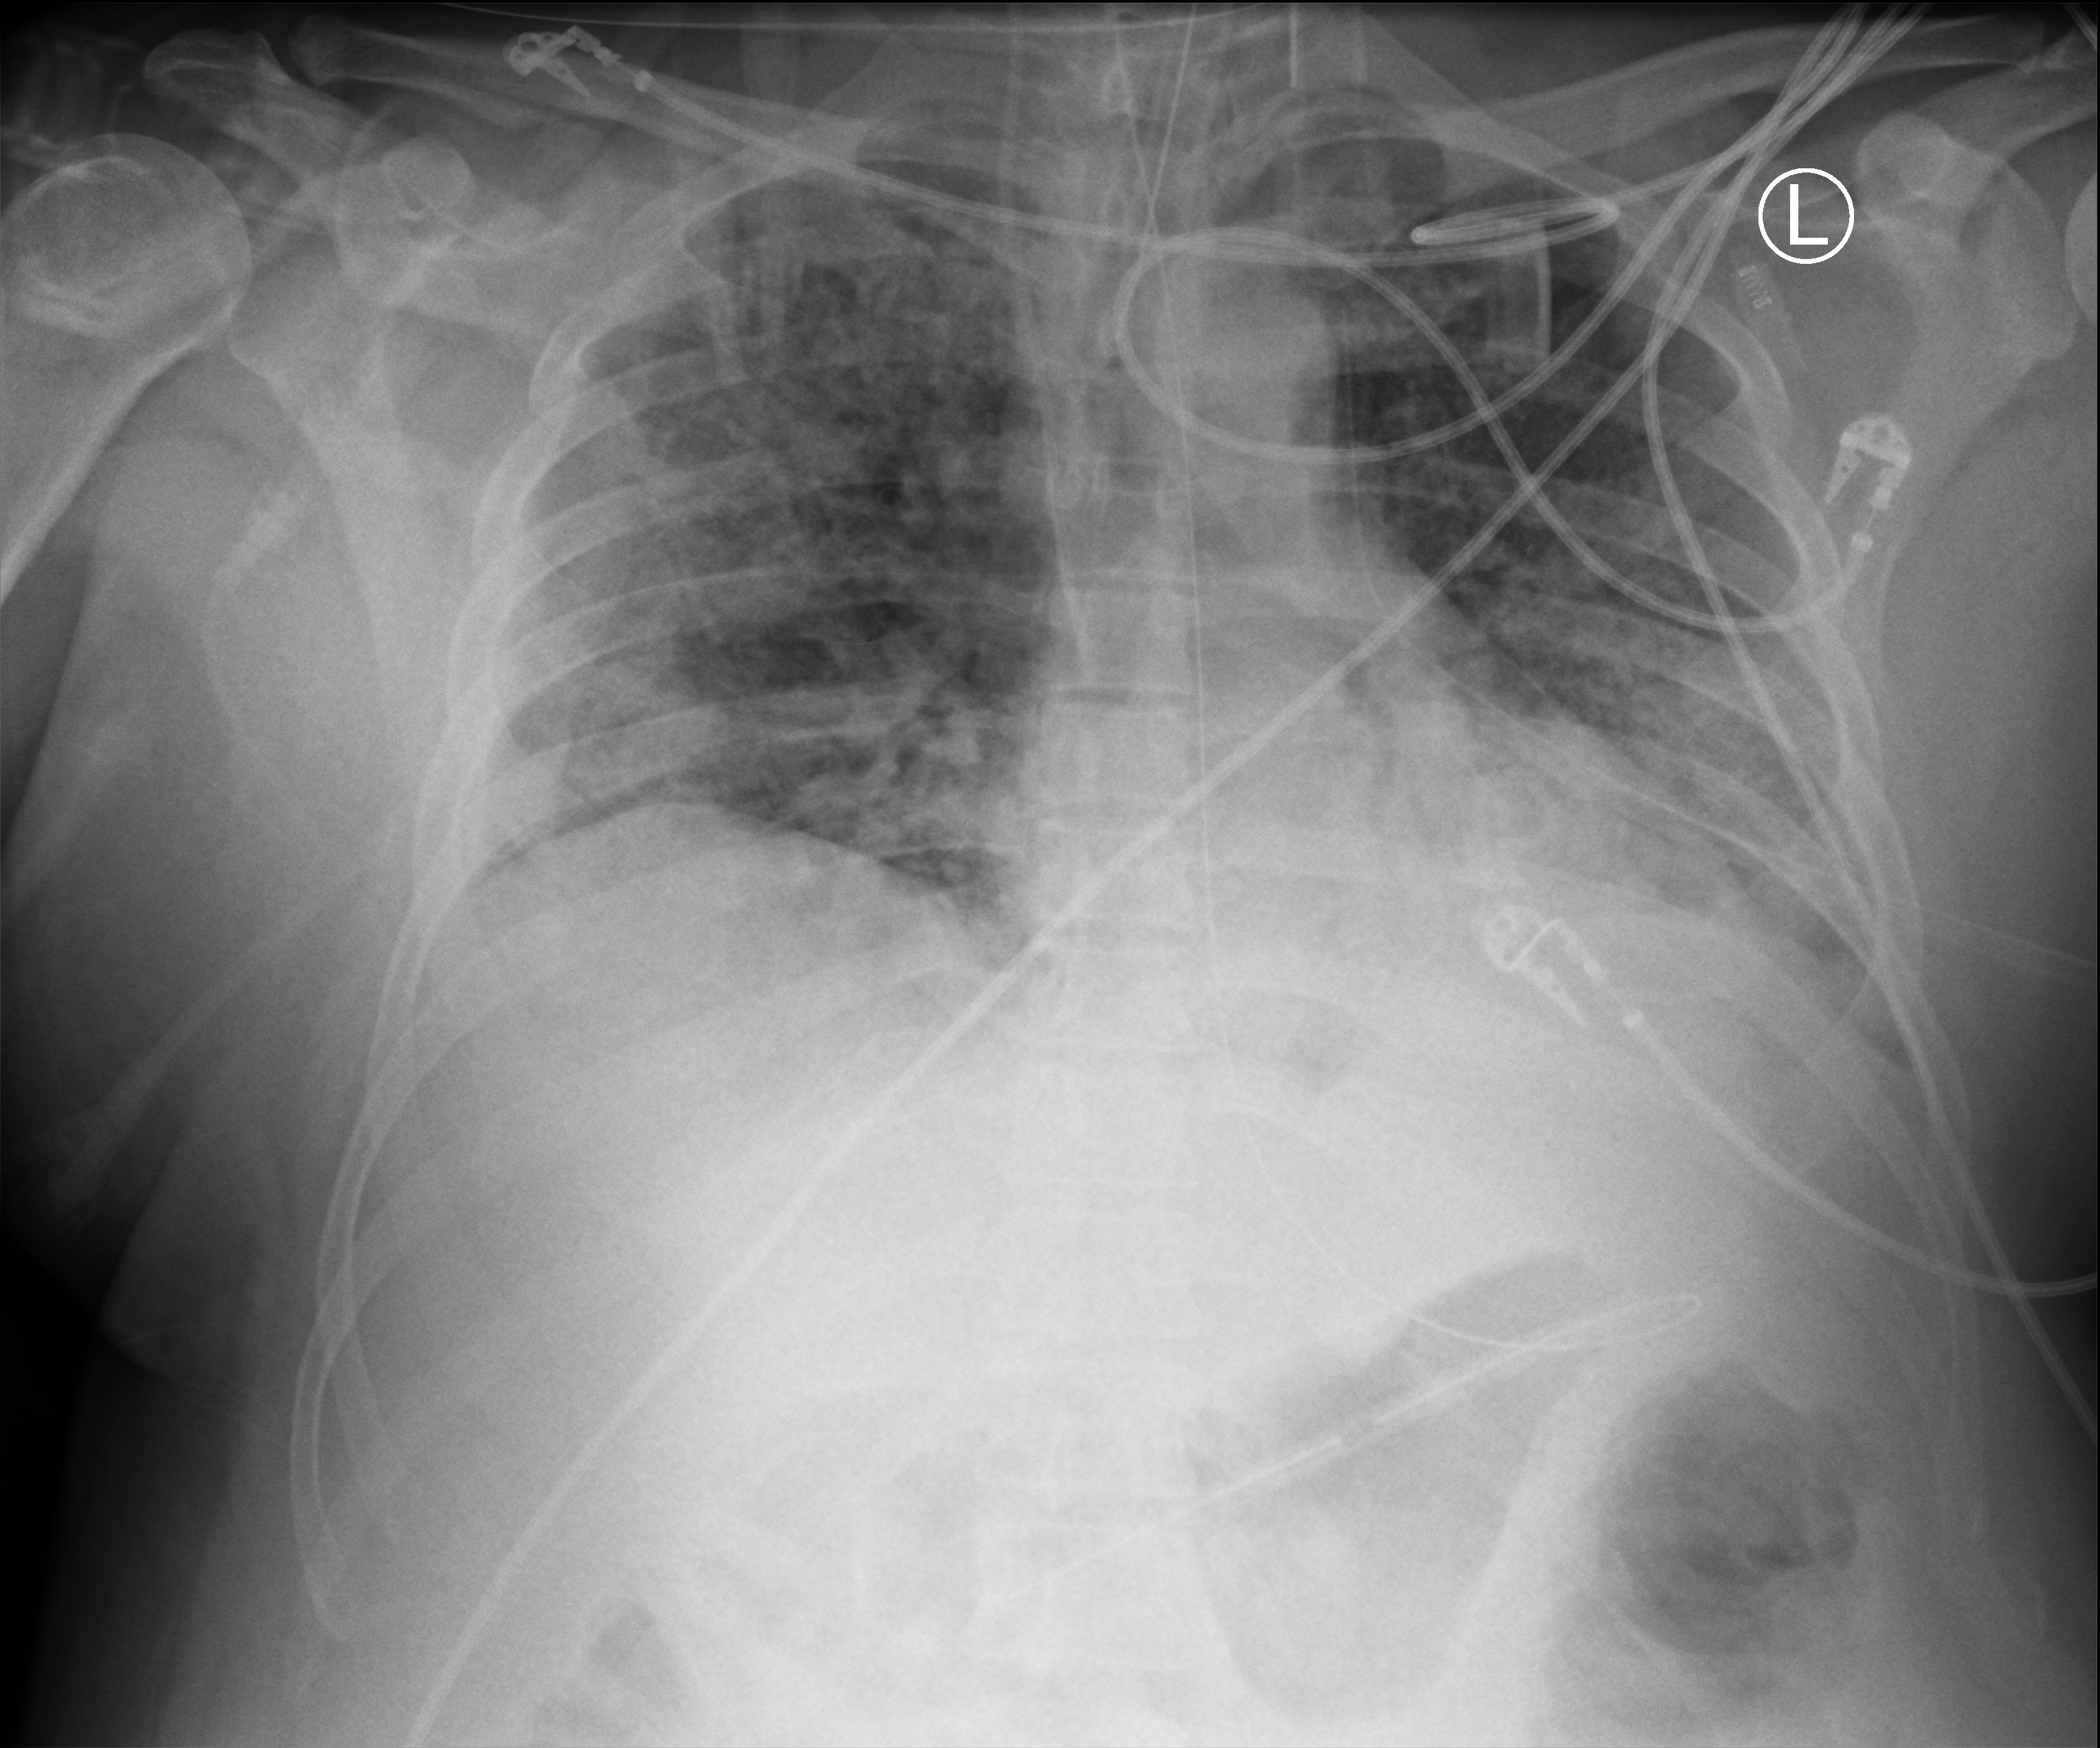
Chest X-ray (portable), anteroposterior (AP) projection. Male patient hospitalised with COVID-19, age 18–59 years.
From the hospital-stay record, not from the radiograph (when in the stay this image was taken is not recorded): length of hospital stay: 96 days.